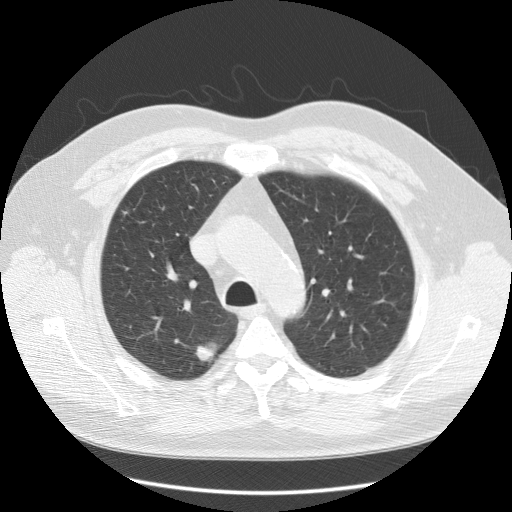
Low-dose screening chest CT, one axial slice; slice 93 of 125 in the series (ordered by position); reconstruction kernel STANDARD; 120 kVp; lung window (W 1500 / L -600 HU); 2.5 mm slice thickness; 512 × 512 image matrix, field of view 380 × 380 mm.
Structures marked on this image (outlined manually by an expert reader):
- lesion 1 (tumor, upper lobe of right lung): bounding box <195,345,216,361> (left, top, right, bottom; pixels)